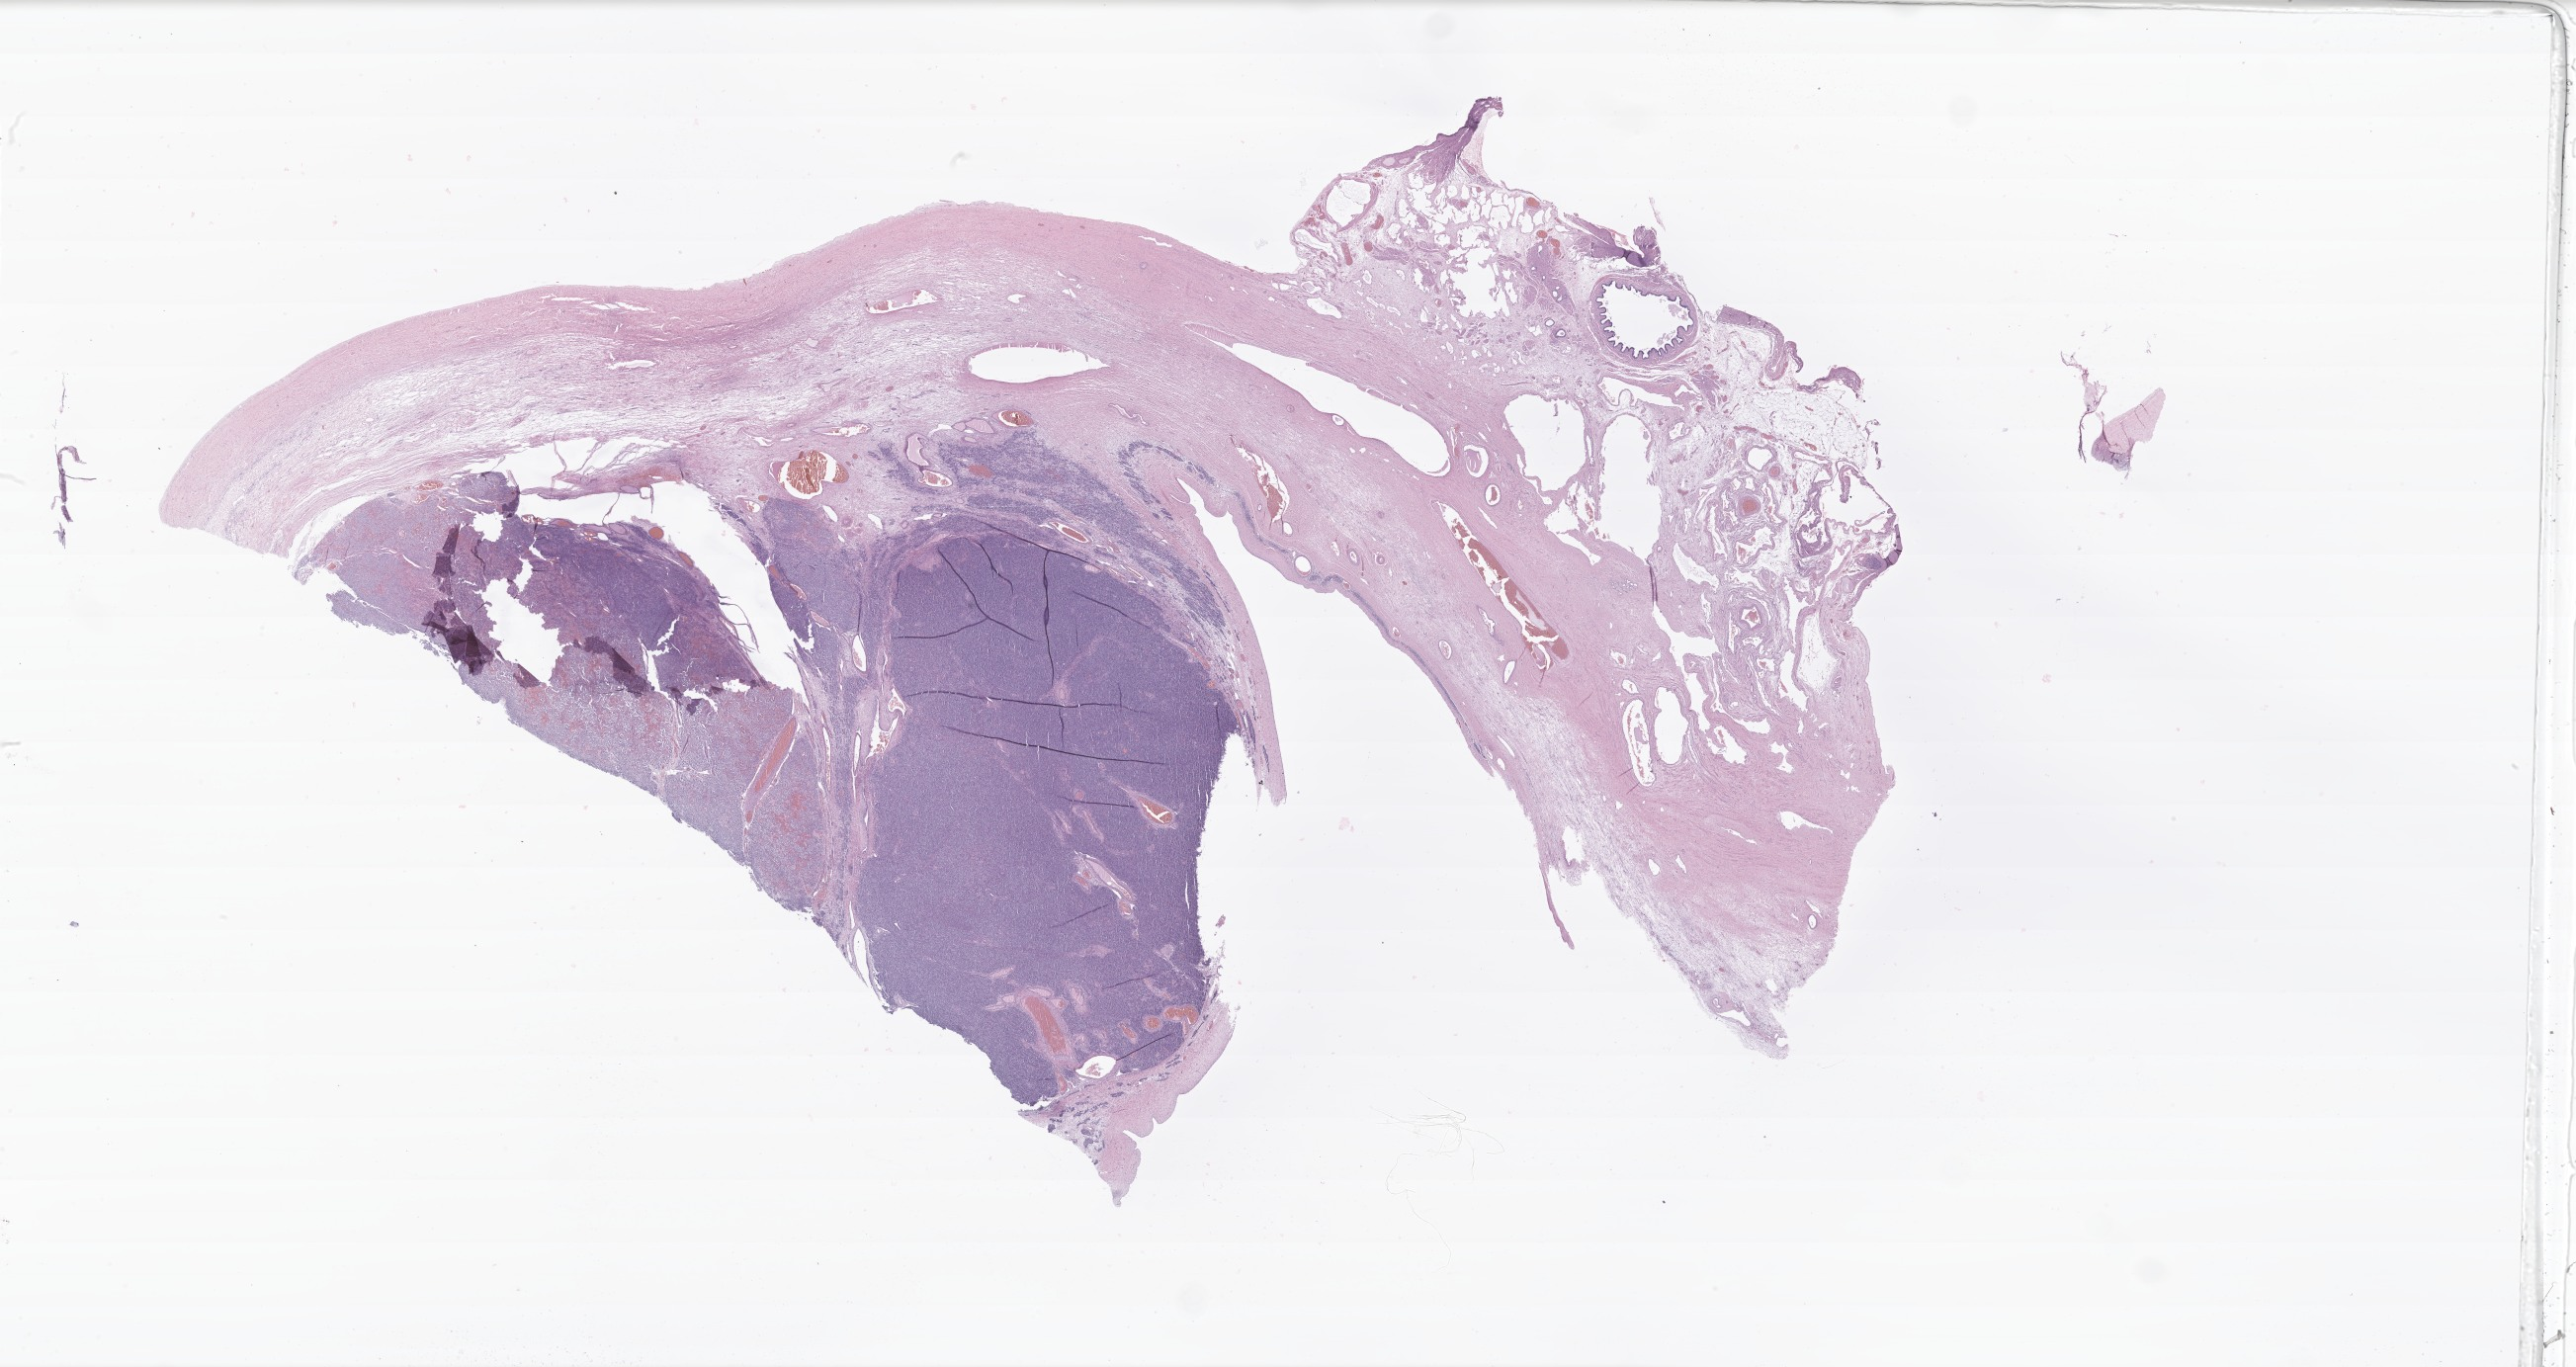
Whole-slide image, haematoxylin and eosin stain of tumor tissue from the ovary, low-resolution overview of the scanned area, about 43.8 x 23.3 mm; formalin-fixed, paraffin-embedded (FFPE) tissue. Patient: female, age 170 months (14 years 2 months).
Diagnosis (ICD-O-3 morphology term): Sex cord-gonadal stromal tumor, mixed forms.